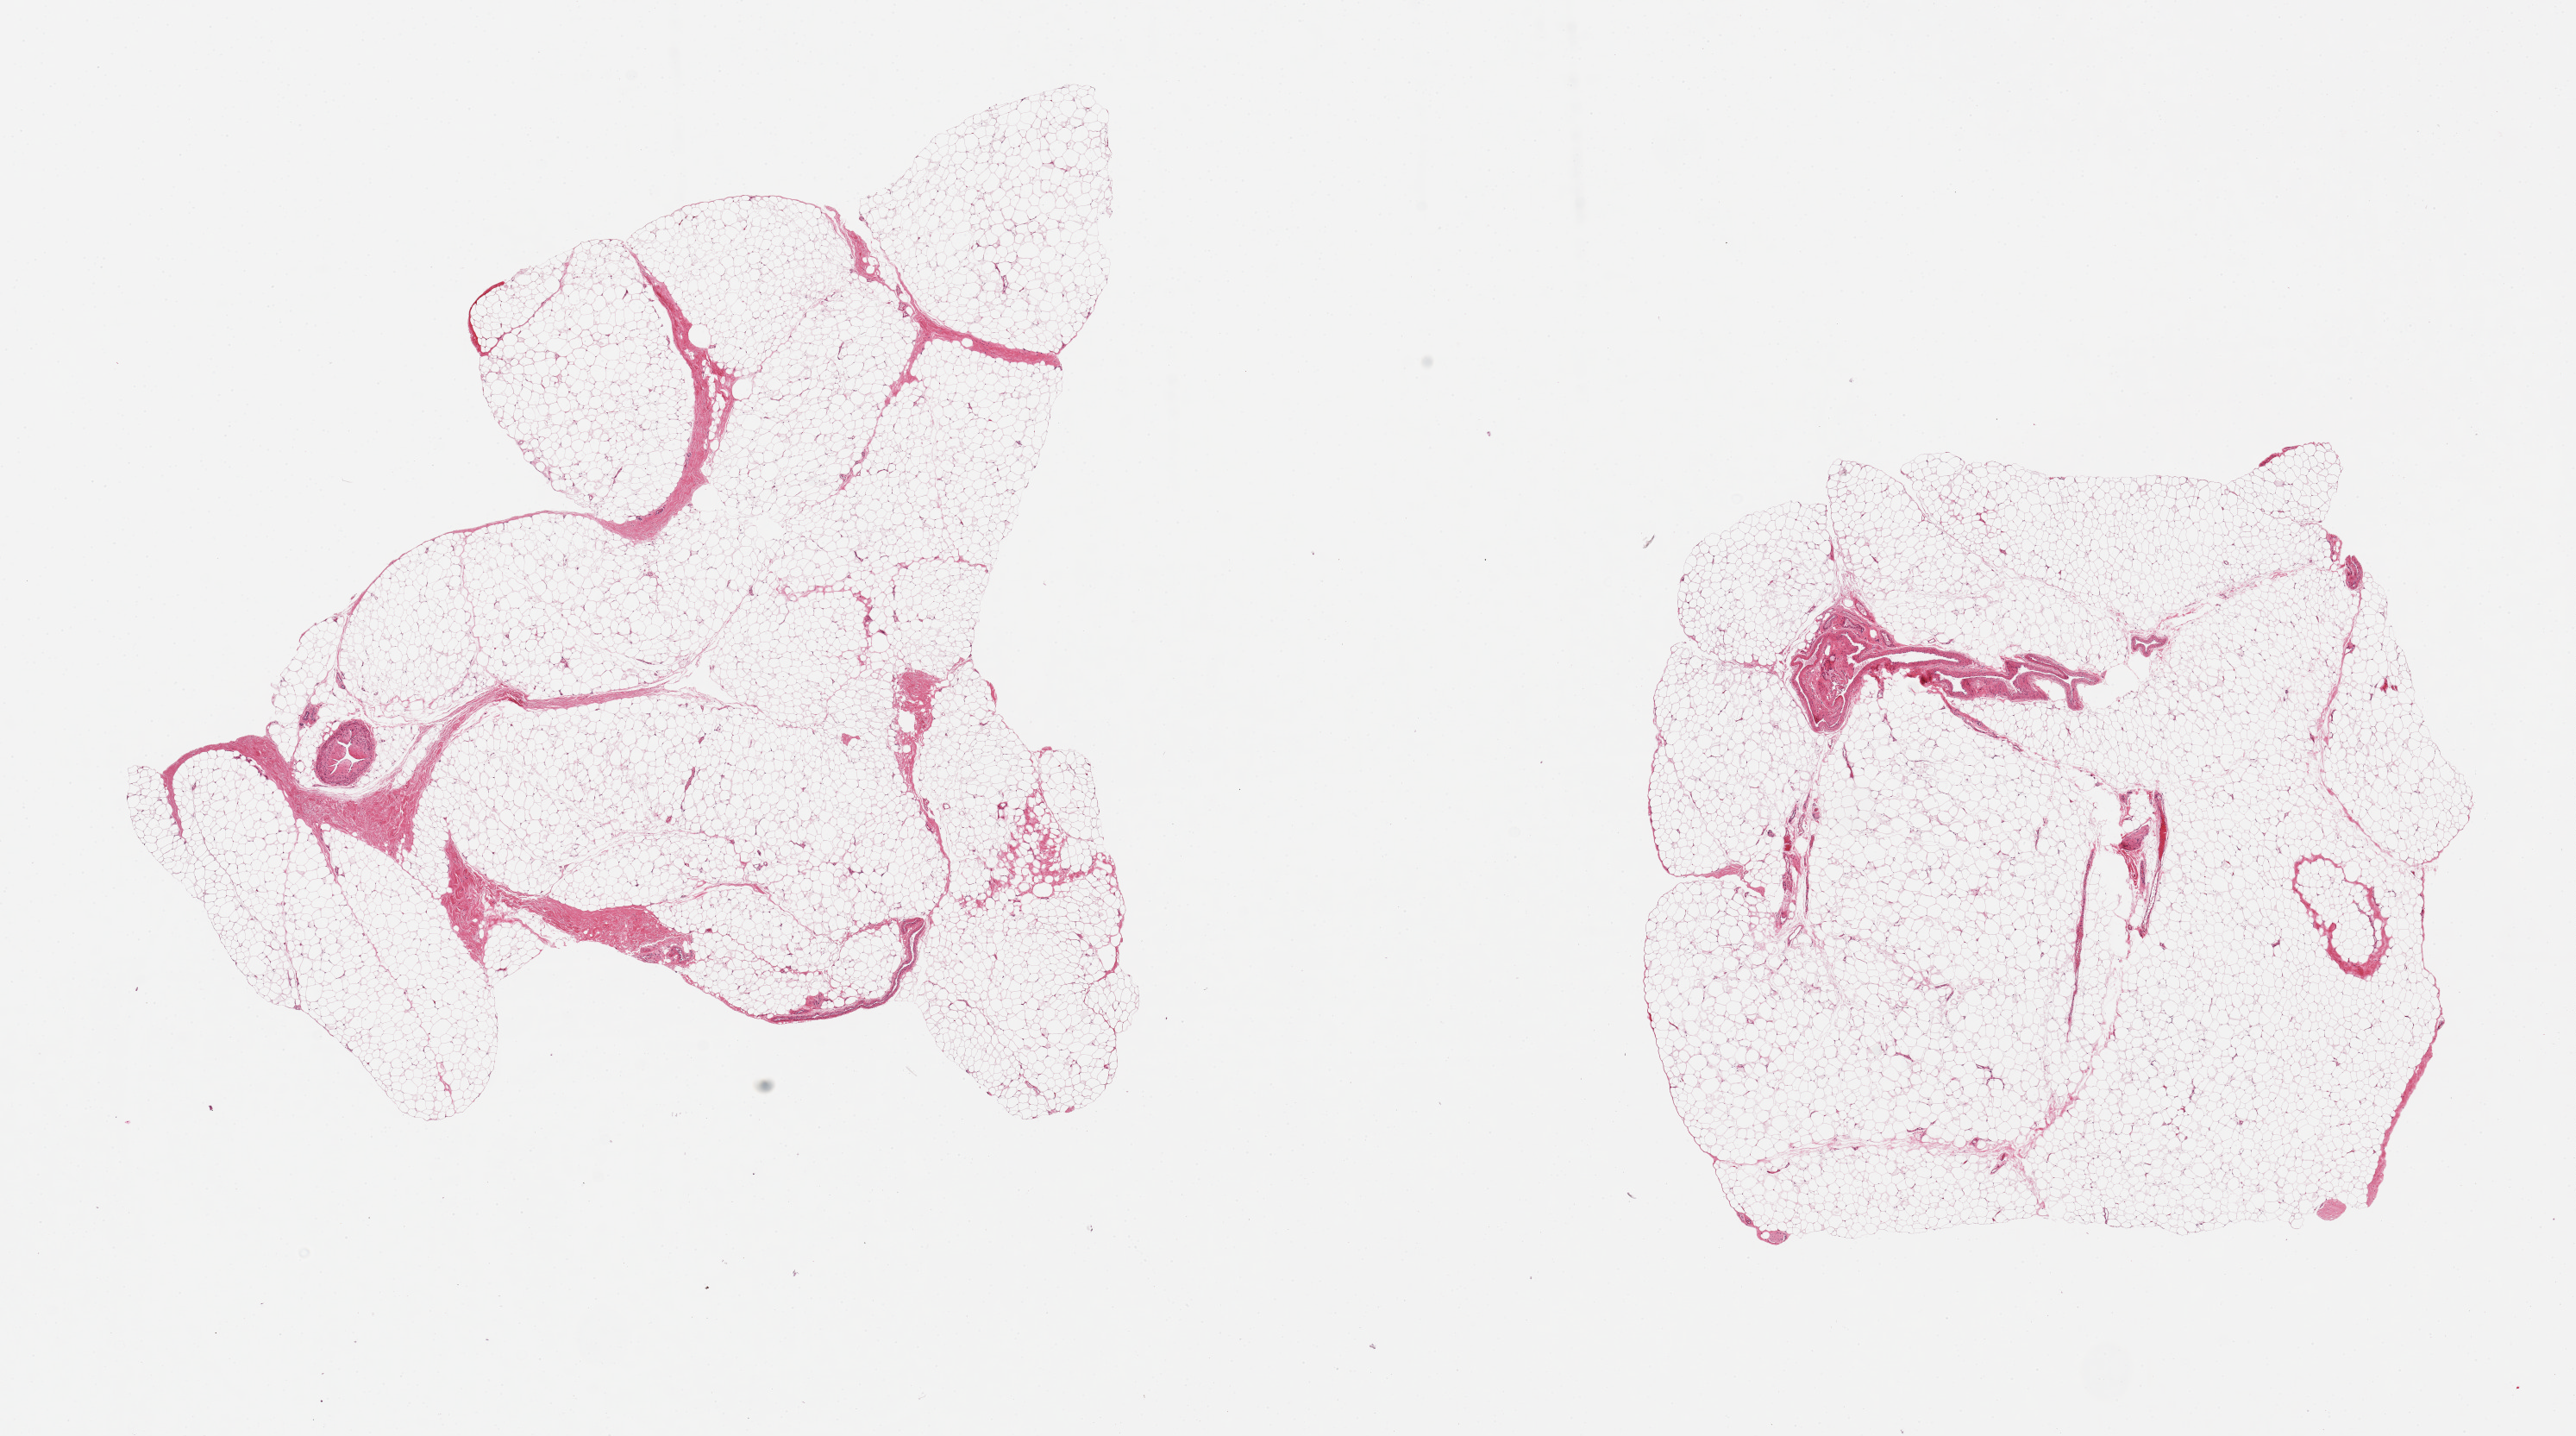
Digitized haematoxylin and eosin-stained section — shown as a low-resolution overview of the whole scanned area (about 23.6 x 13.2 mm). PAXgene-fixed paraffin-embedded (PFPE) section. Section of adipose tissue (target tissue). Donor tissue sample. Male donor.
Review note (as recorded): 2 pieces, ~10-20% fibrous bands/fascia.